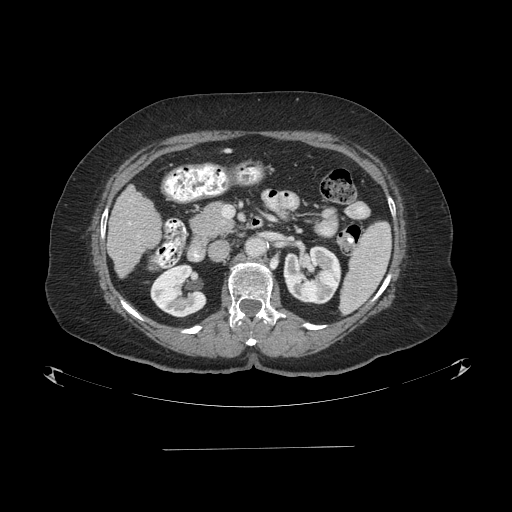
Contrast-enhanced abdominal CT (liver protocol), one axial slice; slice 33 of 103 in the series (ordered by position); reconstruction kernel STANDARD; 120 kVp; one of 2 acquisitions stored at this slice position; soft-tissue window (W 400 / L 40 HU); 512 × 512 image matrix. Case-level facts recorded for this patient, not image findings: diagnosis: hepatocellular carcinoma (patient treated with transarterial chemoembolisation; whether this scan precedes or follows treatment is not stated here); TNM stage (as recorded): Stage-IIIA; Child-Pugh class: A; tumour differentiation: poorly differentiated; tumour nodularity: multinodular.
Structures marked on this image (semi-automatic segmentation, software-assisted and operator-edited):
- liver parenchyma outside the tumour (the mass and vessels are separate outlines, so this box may not span the whole liver): bounding box (x1, y1, x2, y2) in pixels: (106, 186, 160, 278)